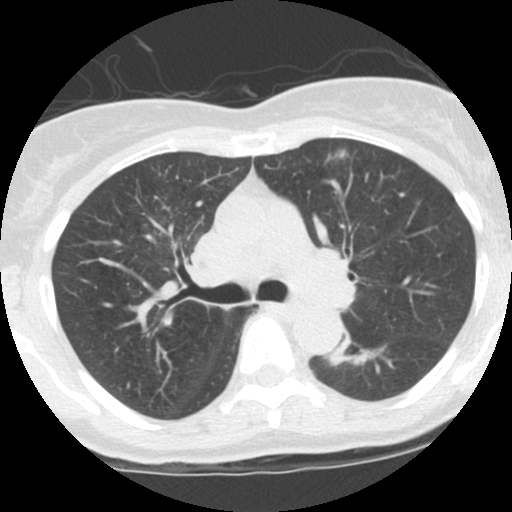
Low-dose screening chest CT, one axial slice. Position 71 of 115 along the scan axis. Reconstruction kernel STANDARD. 120 kVp. Lung window (W 1500 / L -600 HU). 2.5 mm slice thickness. 512 × 512 image matrix, field of view 290 × 290 mm.
Structures marked on this image (manually delineated by an expert):
- lesion 1 (tumor, lower lobe of left lung): bounding box (x1, y1, x2, y2) in pixels: (329, 345, 373, 365)